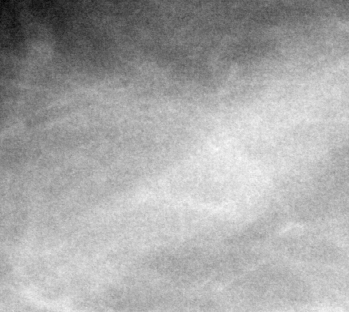
Region of interest cut from a scanned film mammogram (one marked finding); right breast; MLO view; BI-RADS breast density category 1 (scale 1–4).
Finding: mass, shape round, margins circumscribed; BI-RADS assessment category 2; pathology result (as recorded, not read from the image): benign.